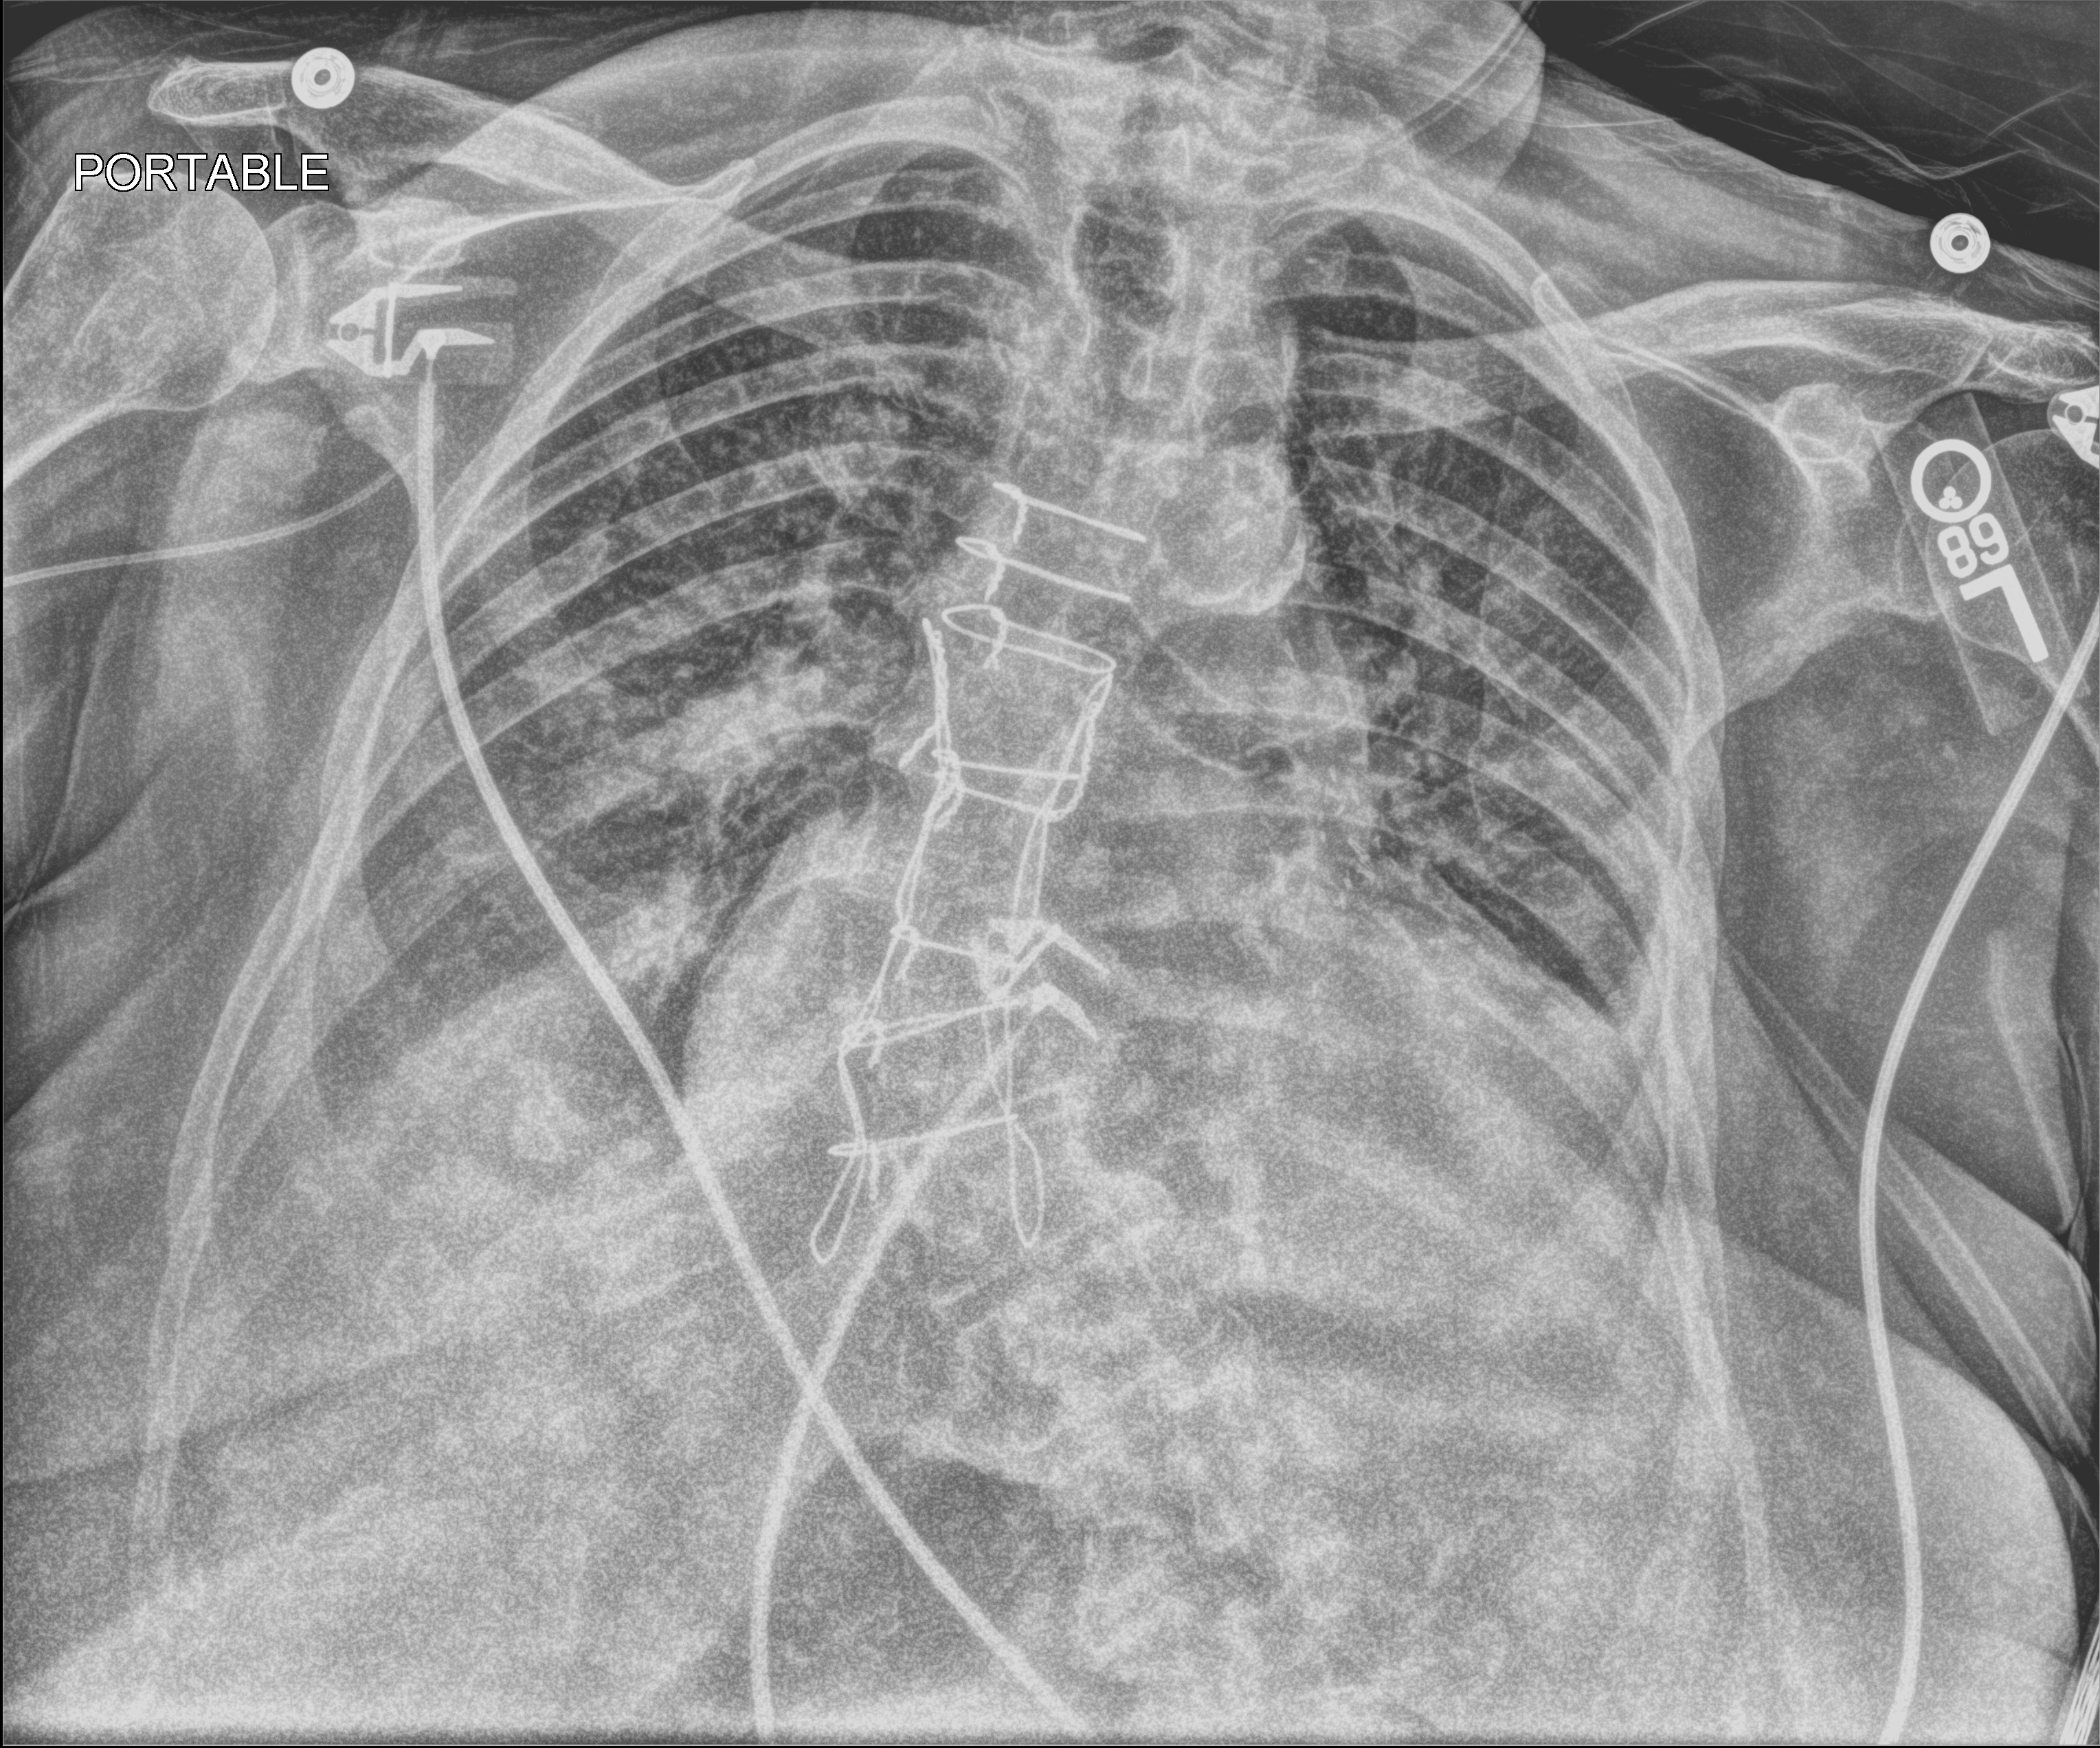
Chest X-ray (portable), anteroposterior (AP) projection. Female patient hospitalised with COVID-19, age 75–90 years.
Hospital-stay facts (about this admission, not read from this image; timing relative to this image not recorded):
- admitted to intensive care during this hospital stay: no